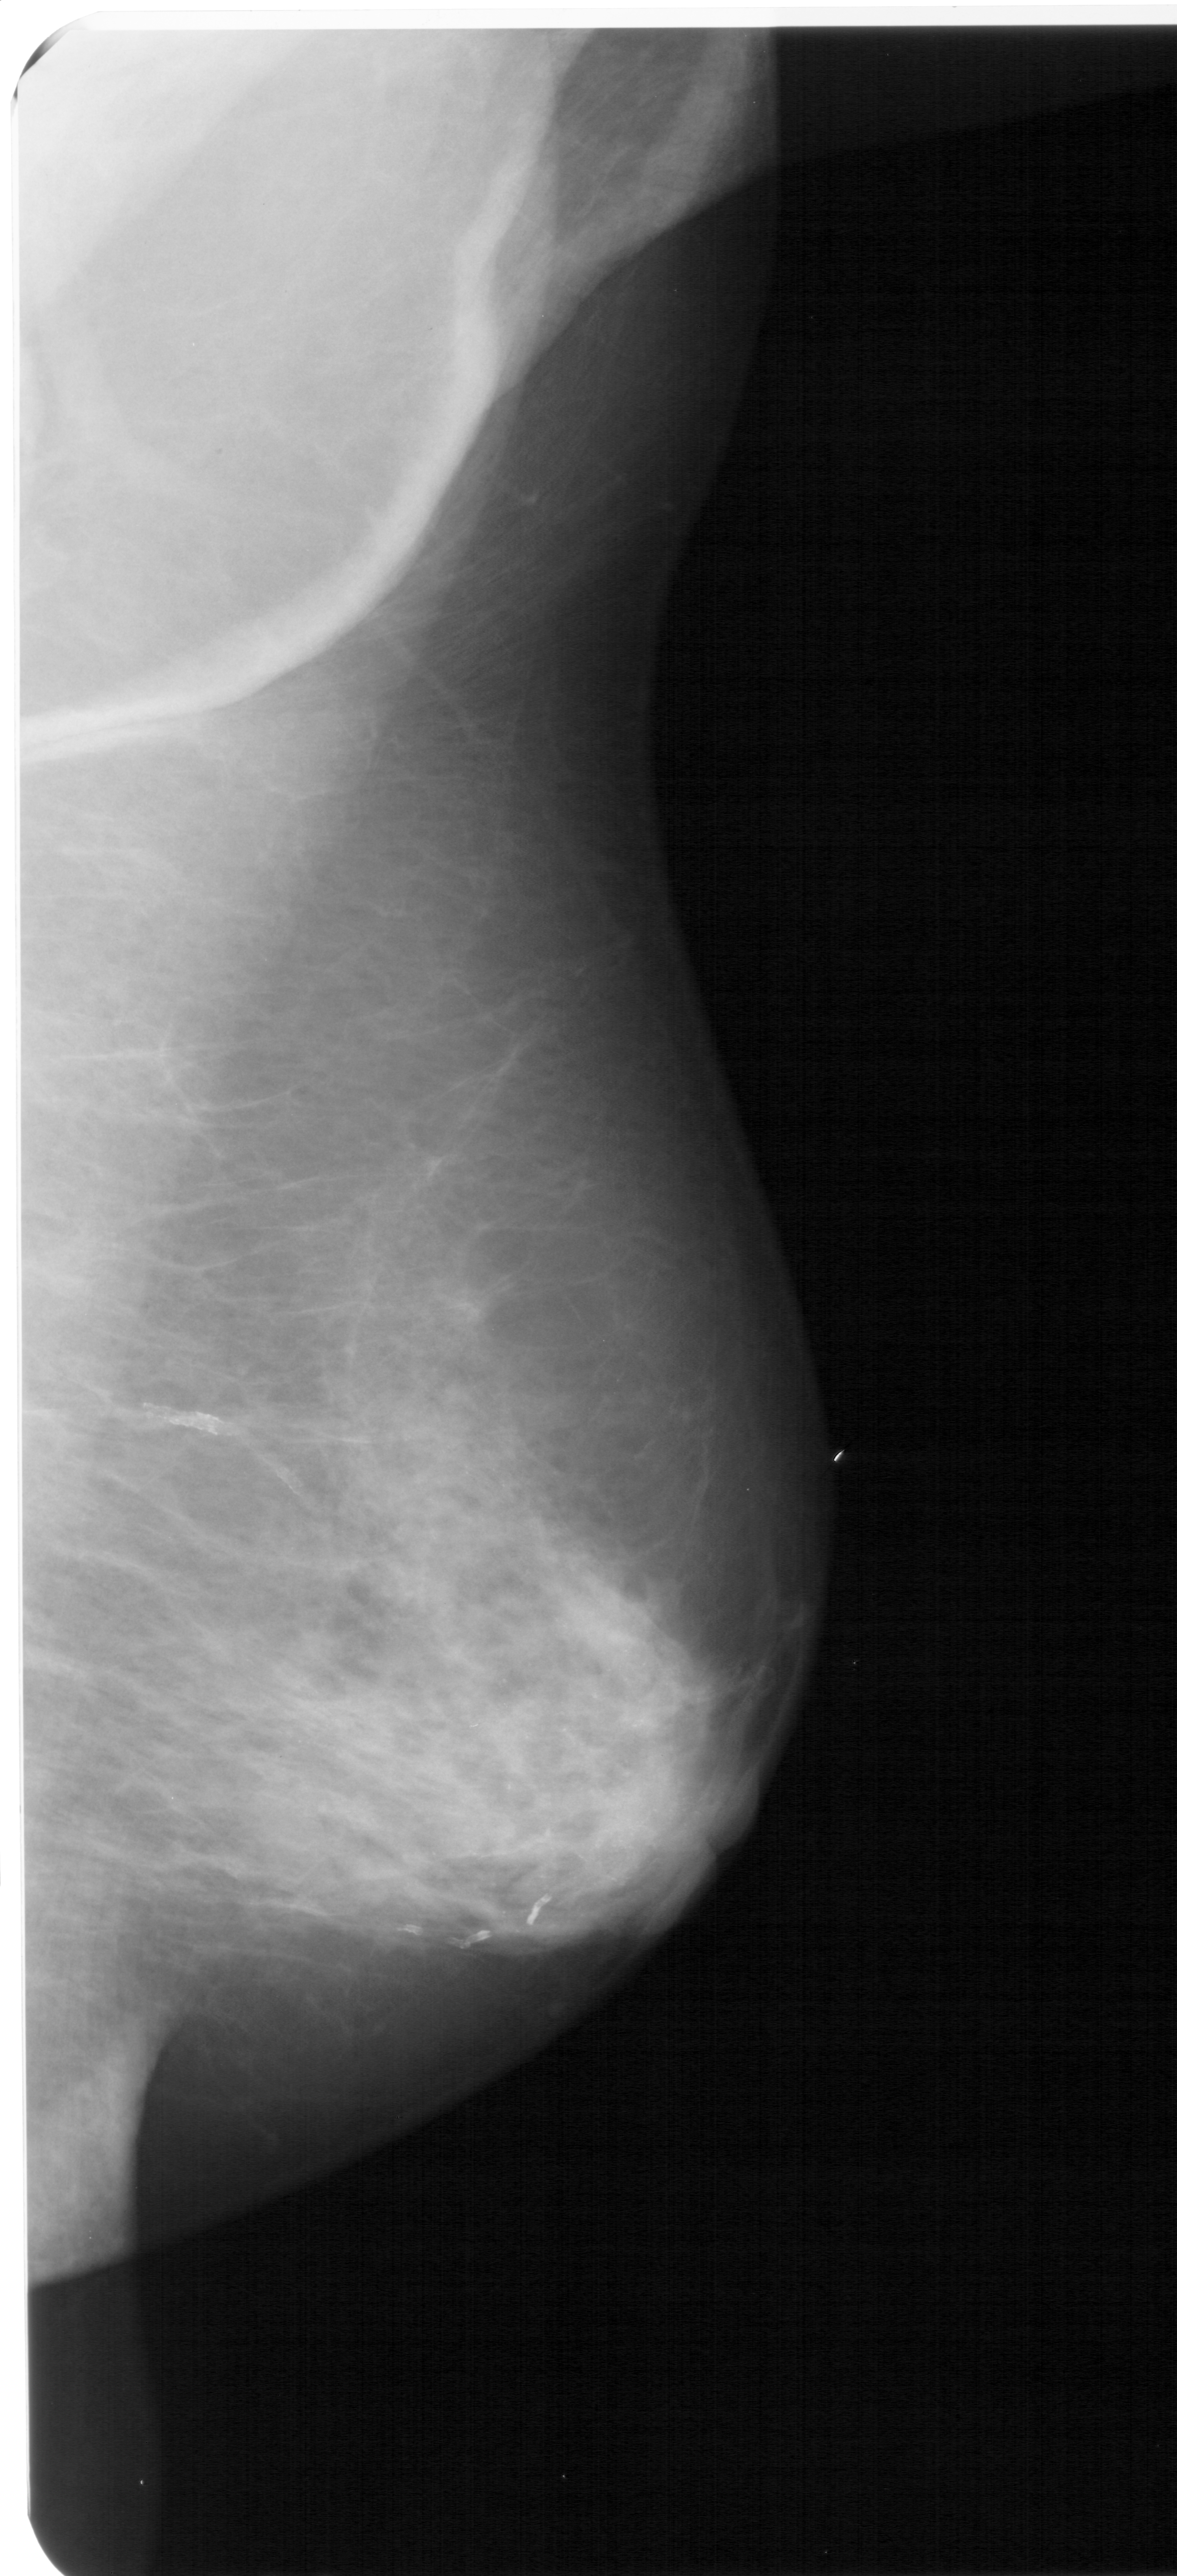
Digitized screen-film mammogram, right breast, MLO view, BI-RADS breast density category 4 (scale 1–4).
Marked abnormality: calcifications, morphology punctate / amorphous, distribution regional; BI-RADS assessment category 4; pathology result (as recorded, not read from the image): benign.